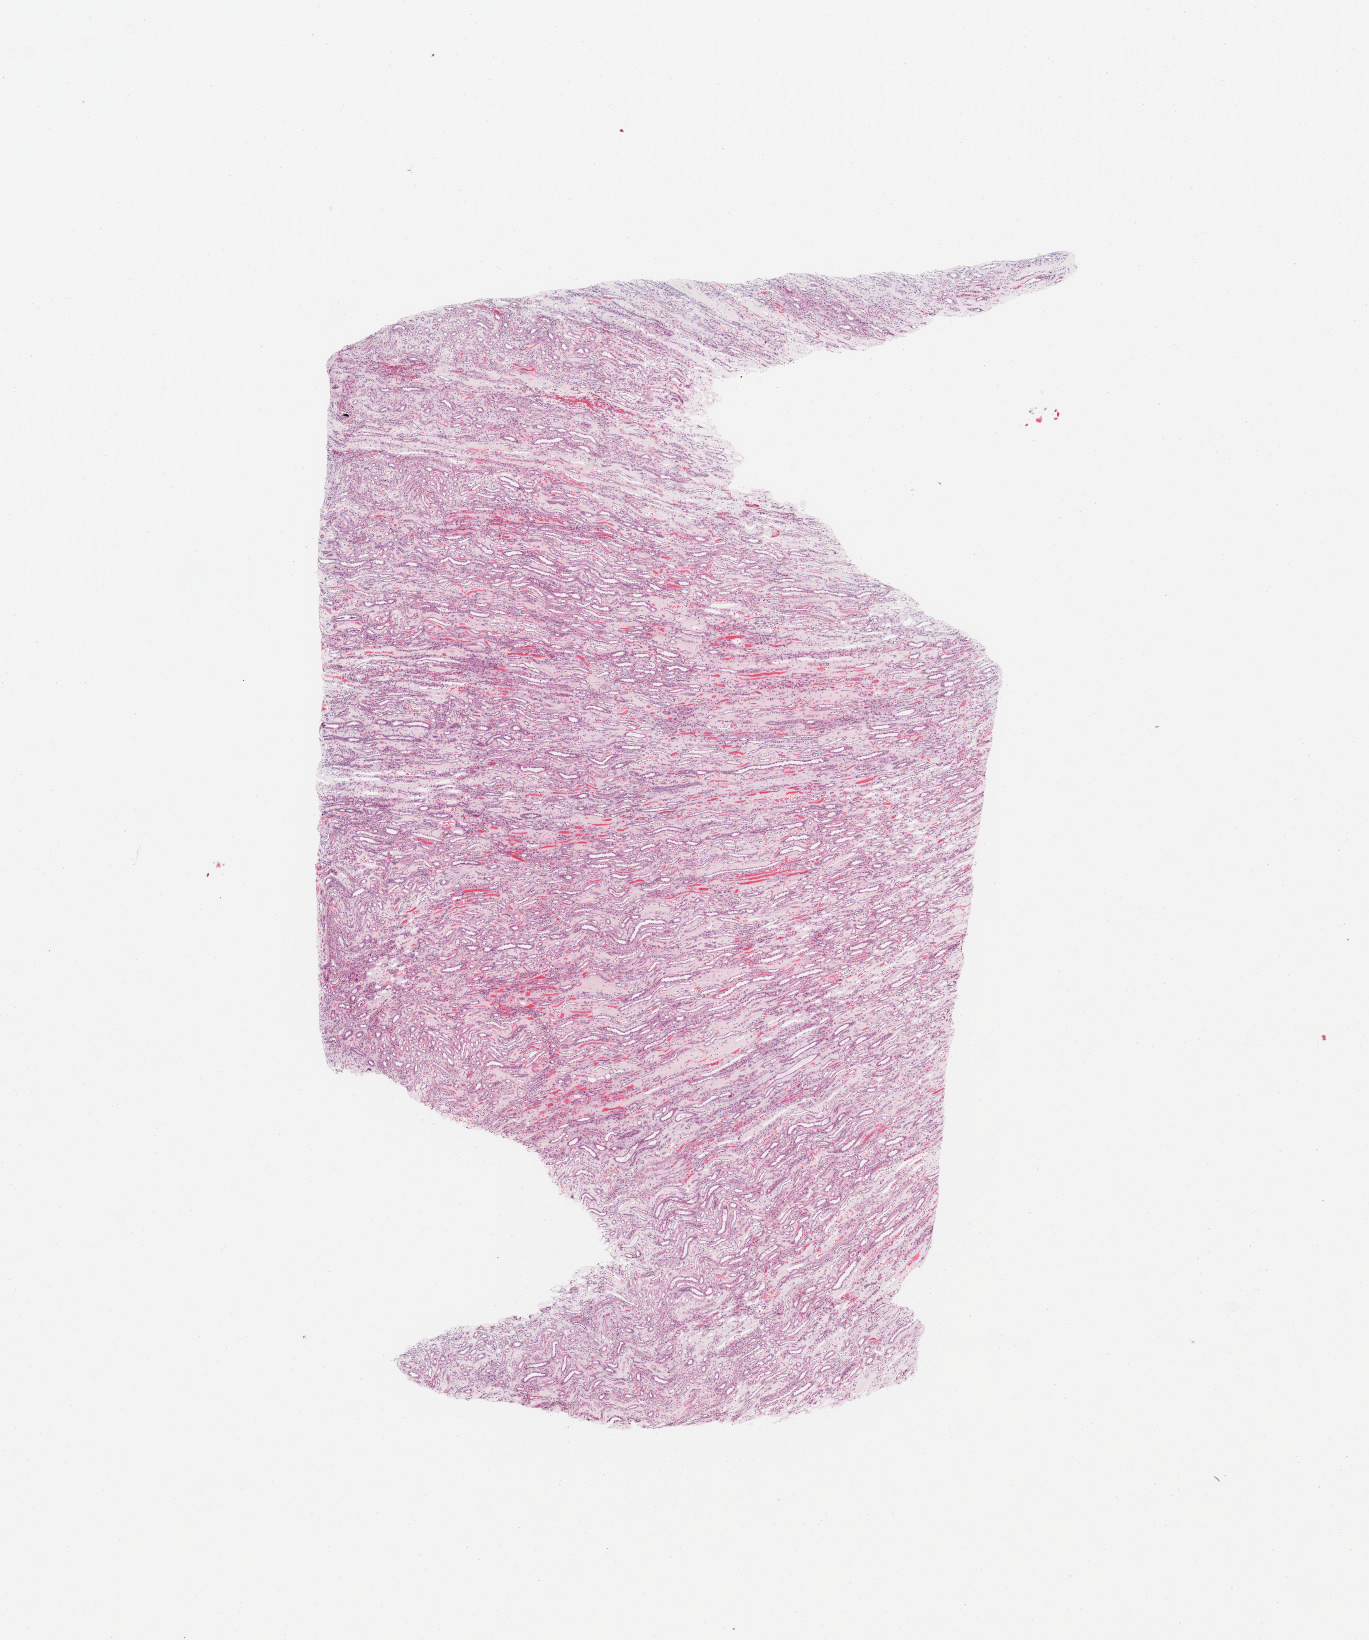
Digitized H&E tissue section (whole slide) — low-resolution overview of the scanned area, about 10.8 x 13.0 mm, normal (non-tumour) tissue sample, sampled site: kidney. 89-year-old male patient.
- this section: normal (non-tumour) tissue from the same patient
- patient diagnosis: Renal cell carcinoma, NOS